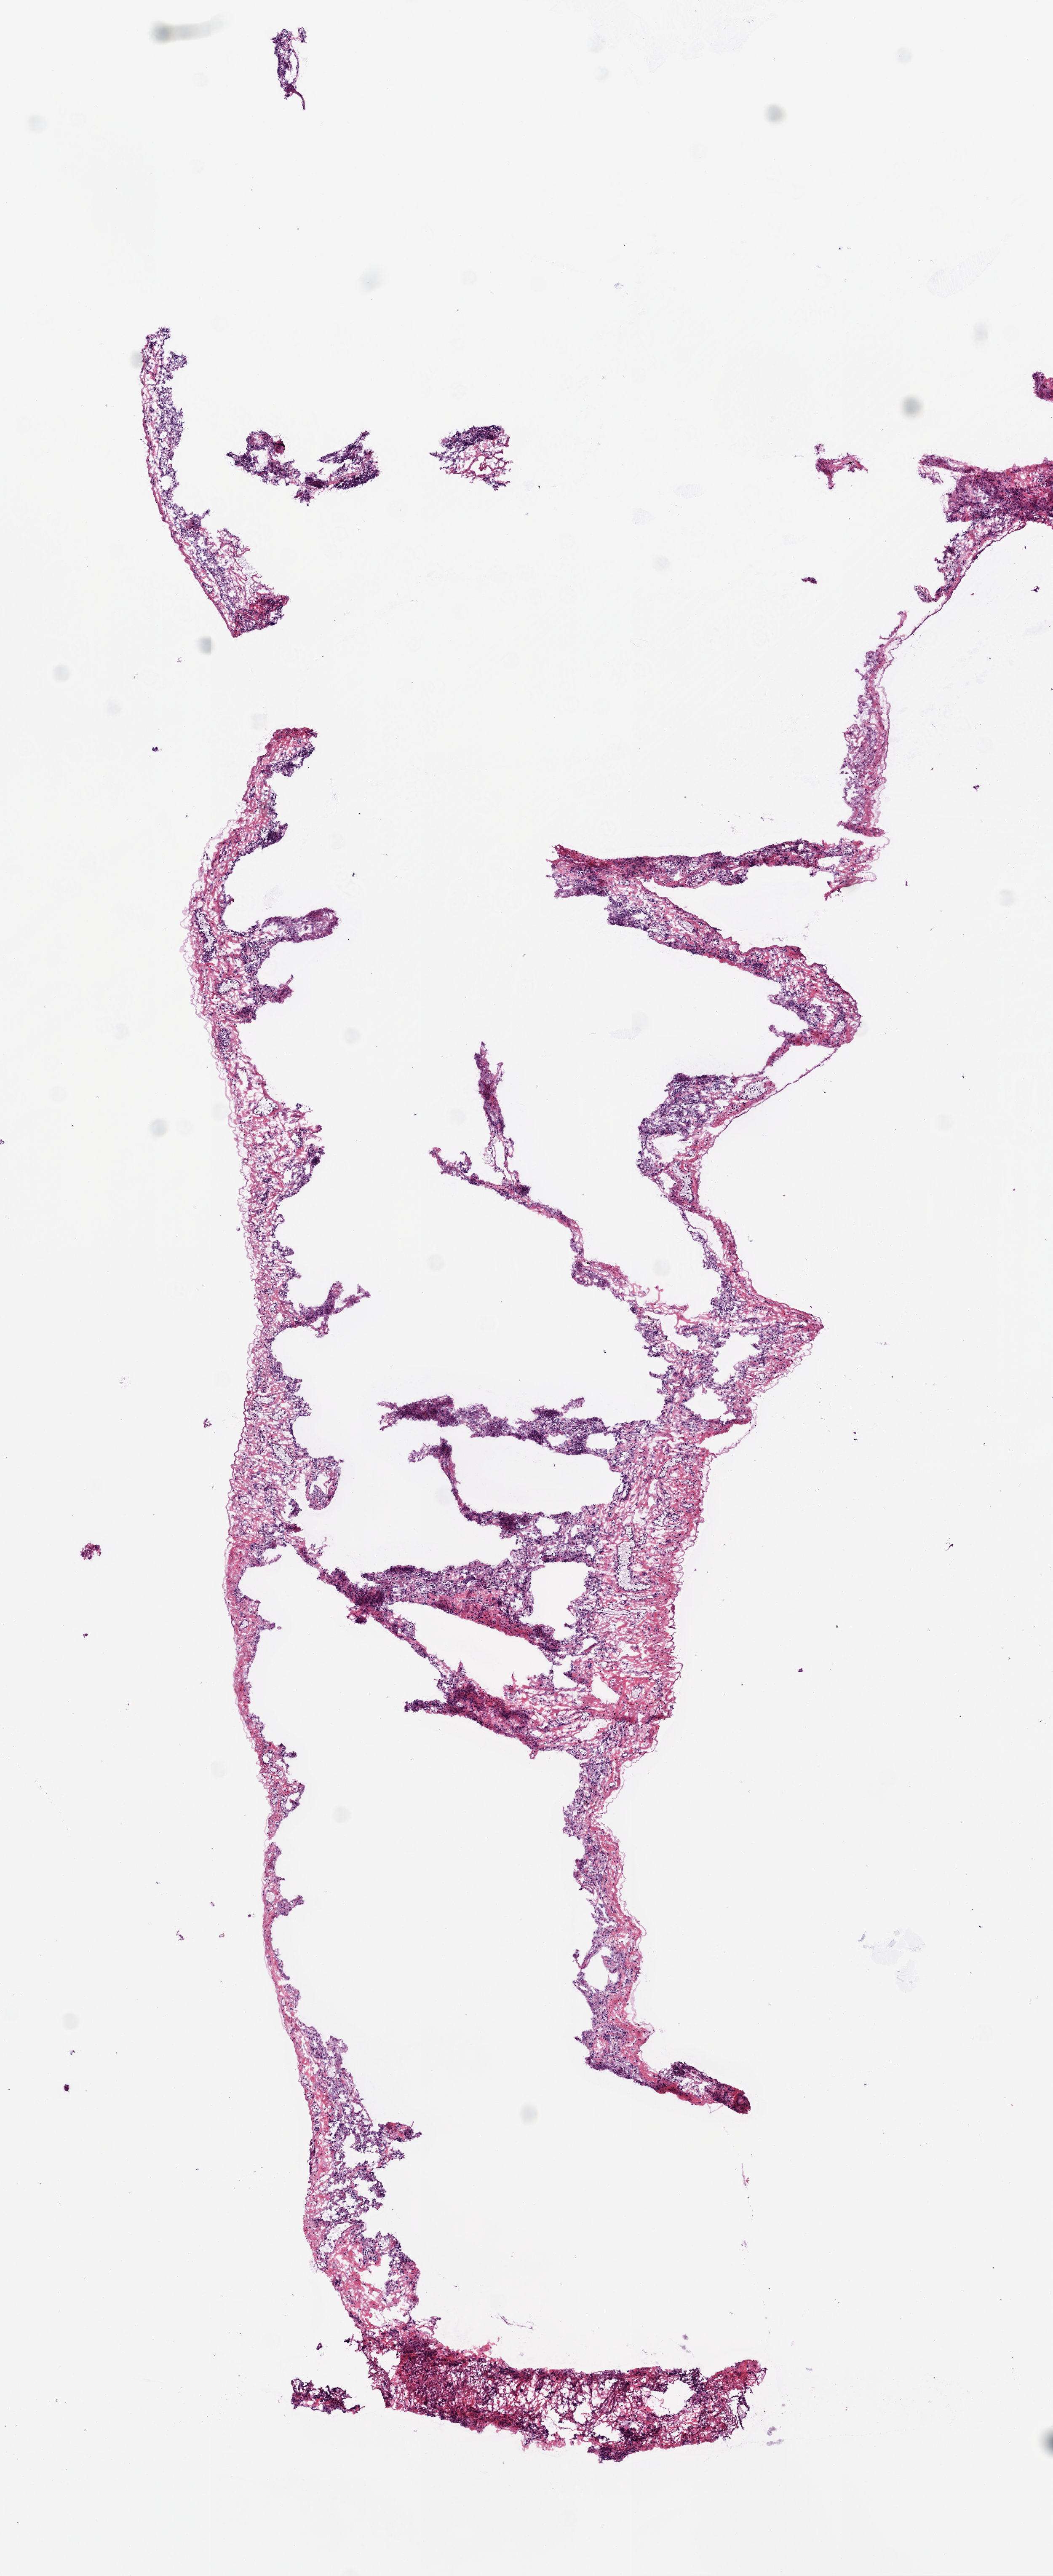
H&E whole-slide image, a low-resolution overview of the entire scanned area, about 5.0 x 12.3 mm (acquisition: 20x scan). Frozen section from the bottom of the tissue portion. Sample: solid tissue normal (non-tumour tissue), lung. Female patient; age at initial diagnosis 68 years.
• this section: solid tissue normal sample (biorepository sample class)
• patient diagnosis: Squamous cell carcinoma, NOS (lower lobe, lung)